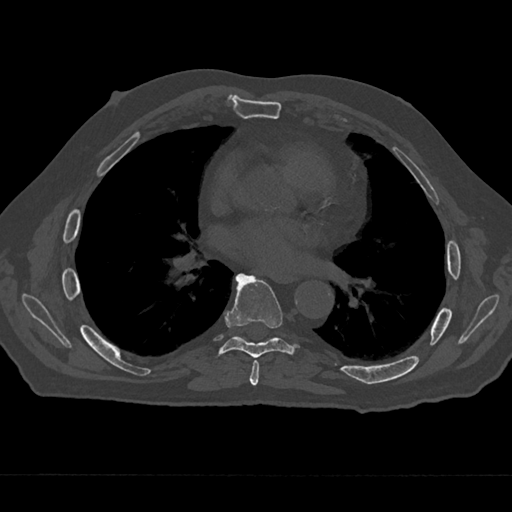
CT including the spine, one axial slice. Position 370 of 797 along the scan axis. Reconstruction kernel Br40s/3. 120 kVp. Bone window (W 1800 / L 400 HU). 512 × 512 image matrix, field of view 377 × 377 mm. Patient: male, 75 years. Case-level facts recorded for this patient, not image findings: primary cancer: renal; vertebrae with lytic lesions (as recorded): T4.
Outlined on this slice (semi-automatically segmented with operator editing):
- T6 vertebra: bounding box (x1, y1, x2, y2) in pixels: (249, 360, 260, 386)
- T7 vertebra: (214, 273, 300, 359)